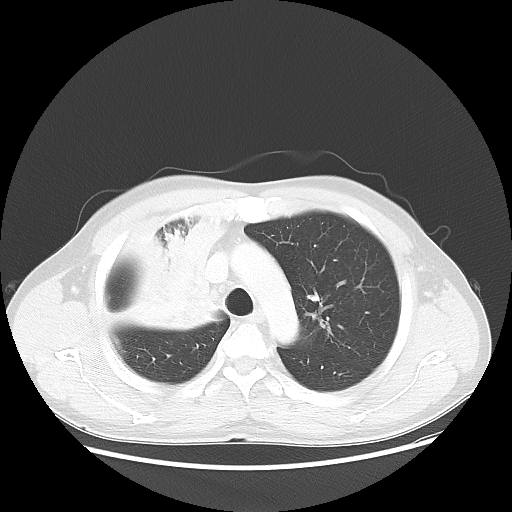
Chest CT, one axial slice; position 40 of 56 along the scan axis; reconstruction kernel LUNG; 100 kVp; lung window (W 1500 / L -600 HU); 512 × 512 image matrix, field of view 398 × 398 mm. Male patient, age 60 years. Case-level facts recorded for this patient, not image findings: clinical TNM (as recorded): T2a N1 M0.
Outlined on this slice (rectangle marked by the reading radiologist):
- lung tumour (recorded histology: squamous cell carcinoma): bounding box <113,195,239,348> (left, top, right, bottom; pixels)